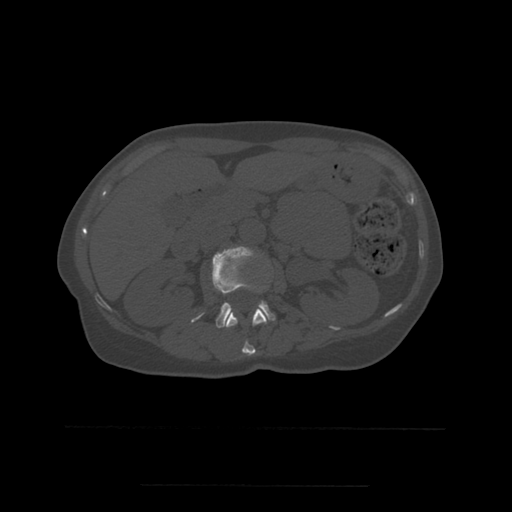
CT including the spine, one axial slice. Slice 223 of 544 in the series (ordered by position). Bone window (W 1800 / L 400 HU). 1.25 mm slice thickness. 512 × 512 image matrix, field of view 350 × 350 mm. Patient age 58 years. Case-level facts recorded for this patient, not image findings: primary cancer: lung.
Outlined on this slice (semi-automatic segmentation, software-assisted and operator-edited):
- L1 vertebra: box from (x=225, y=309) to (x=267, y=356) px
- L2 vertebra: (x=192, y=247)–(x=276, y=328)